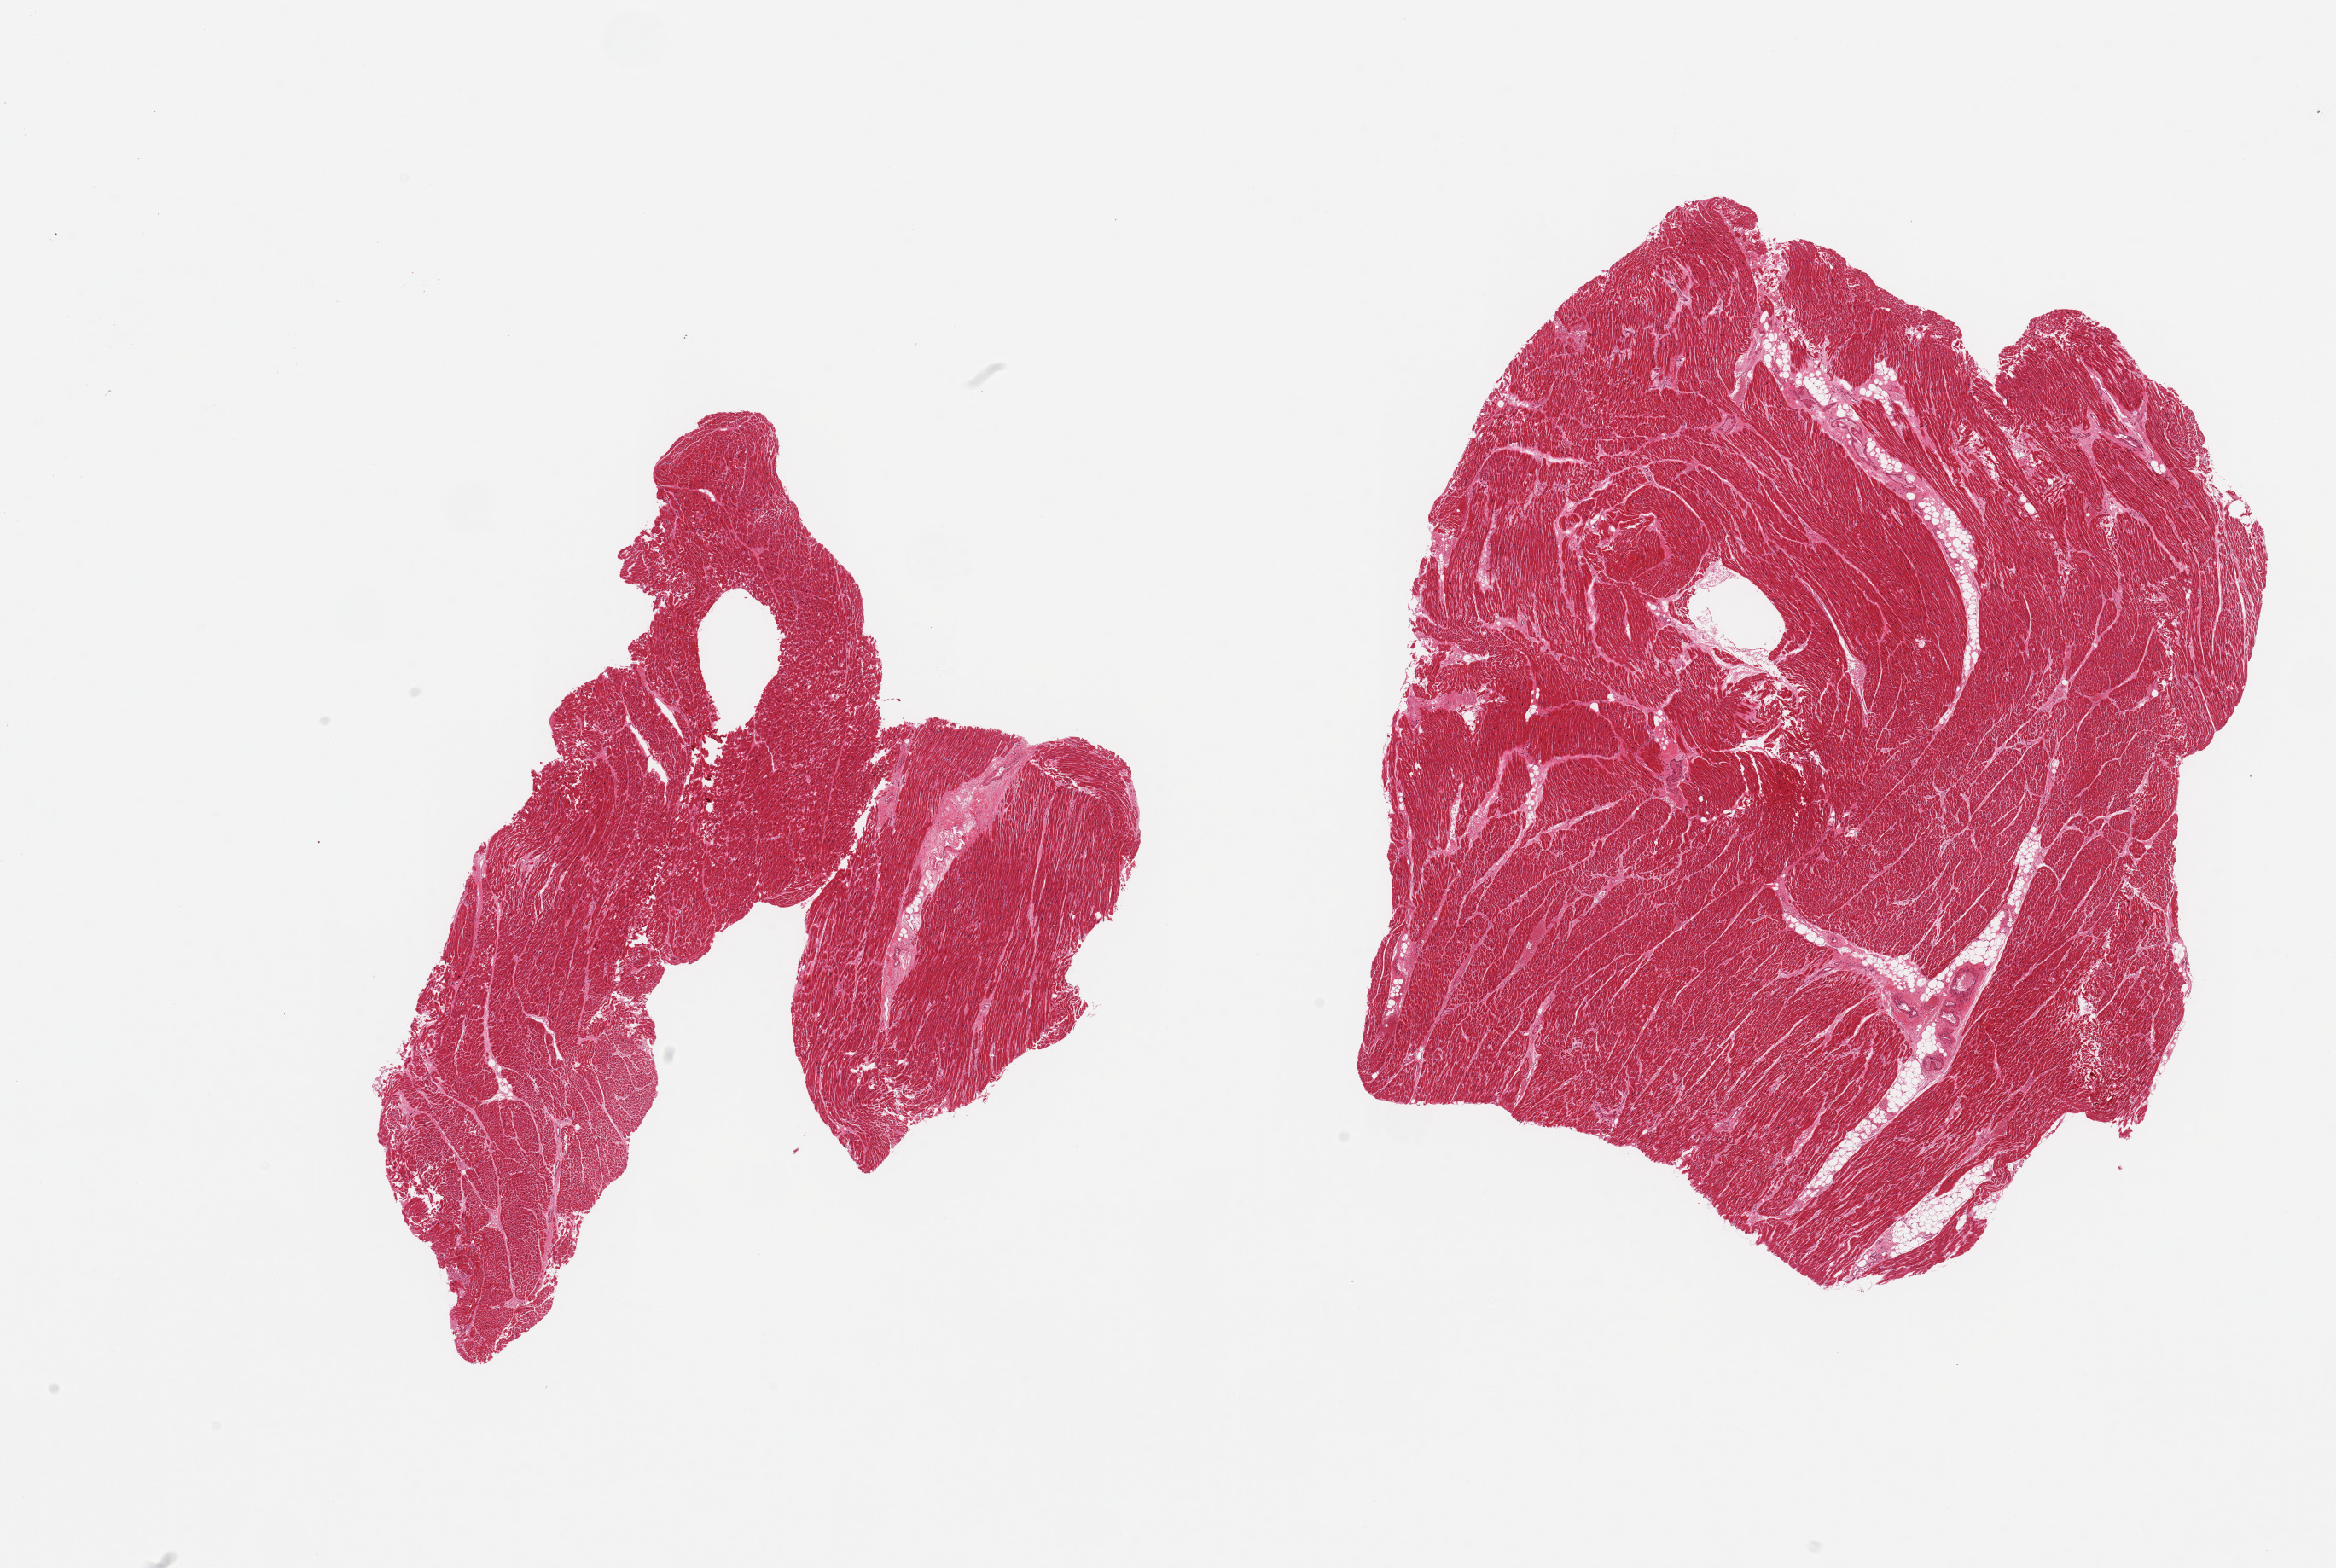
Digitized H&E-stained section, brightfield, low-resolution overview of the scanned area, about 21.7 x 14.5 mm (slide scanned at 20x). PAXgene-fixed paraffin-embedded (PFPE) section. Target tissue: heart. Donor tissue sample. Donor: male.
* review note (as recorded): 2 pieces; some perivascular fat